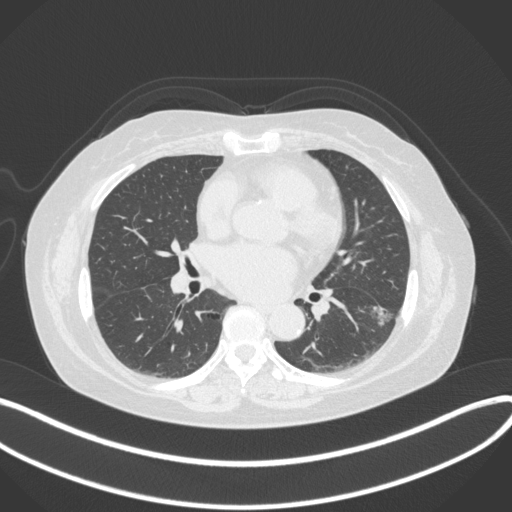
Chest CT, one axial slice; slice 176 of 373 in the series (ordered by position); reconstruction kernel B31f; 120 kVp; lung window (W 1500 / L -600 HU); 512 × 512 image matrix. Patient: female, 67 years. Case-level facts recorded for this patient, not image findings: clinical TNM (as recorded): T1c N0 M0.
Structures marked on this image (bounding box drawn by a radiologist):
- lung tumour (recorded histology: adenocarcinoma): bounding box <362,302,398,332> (left, top, right, bottom; pixels)